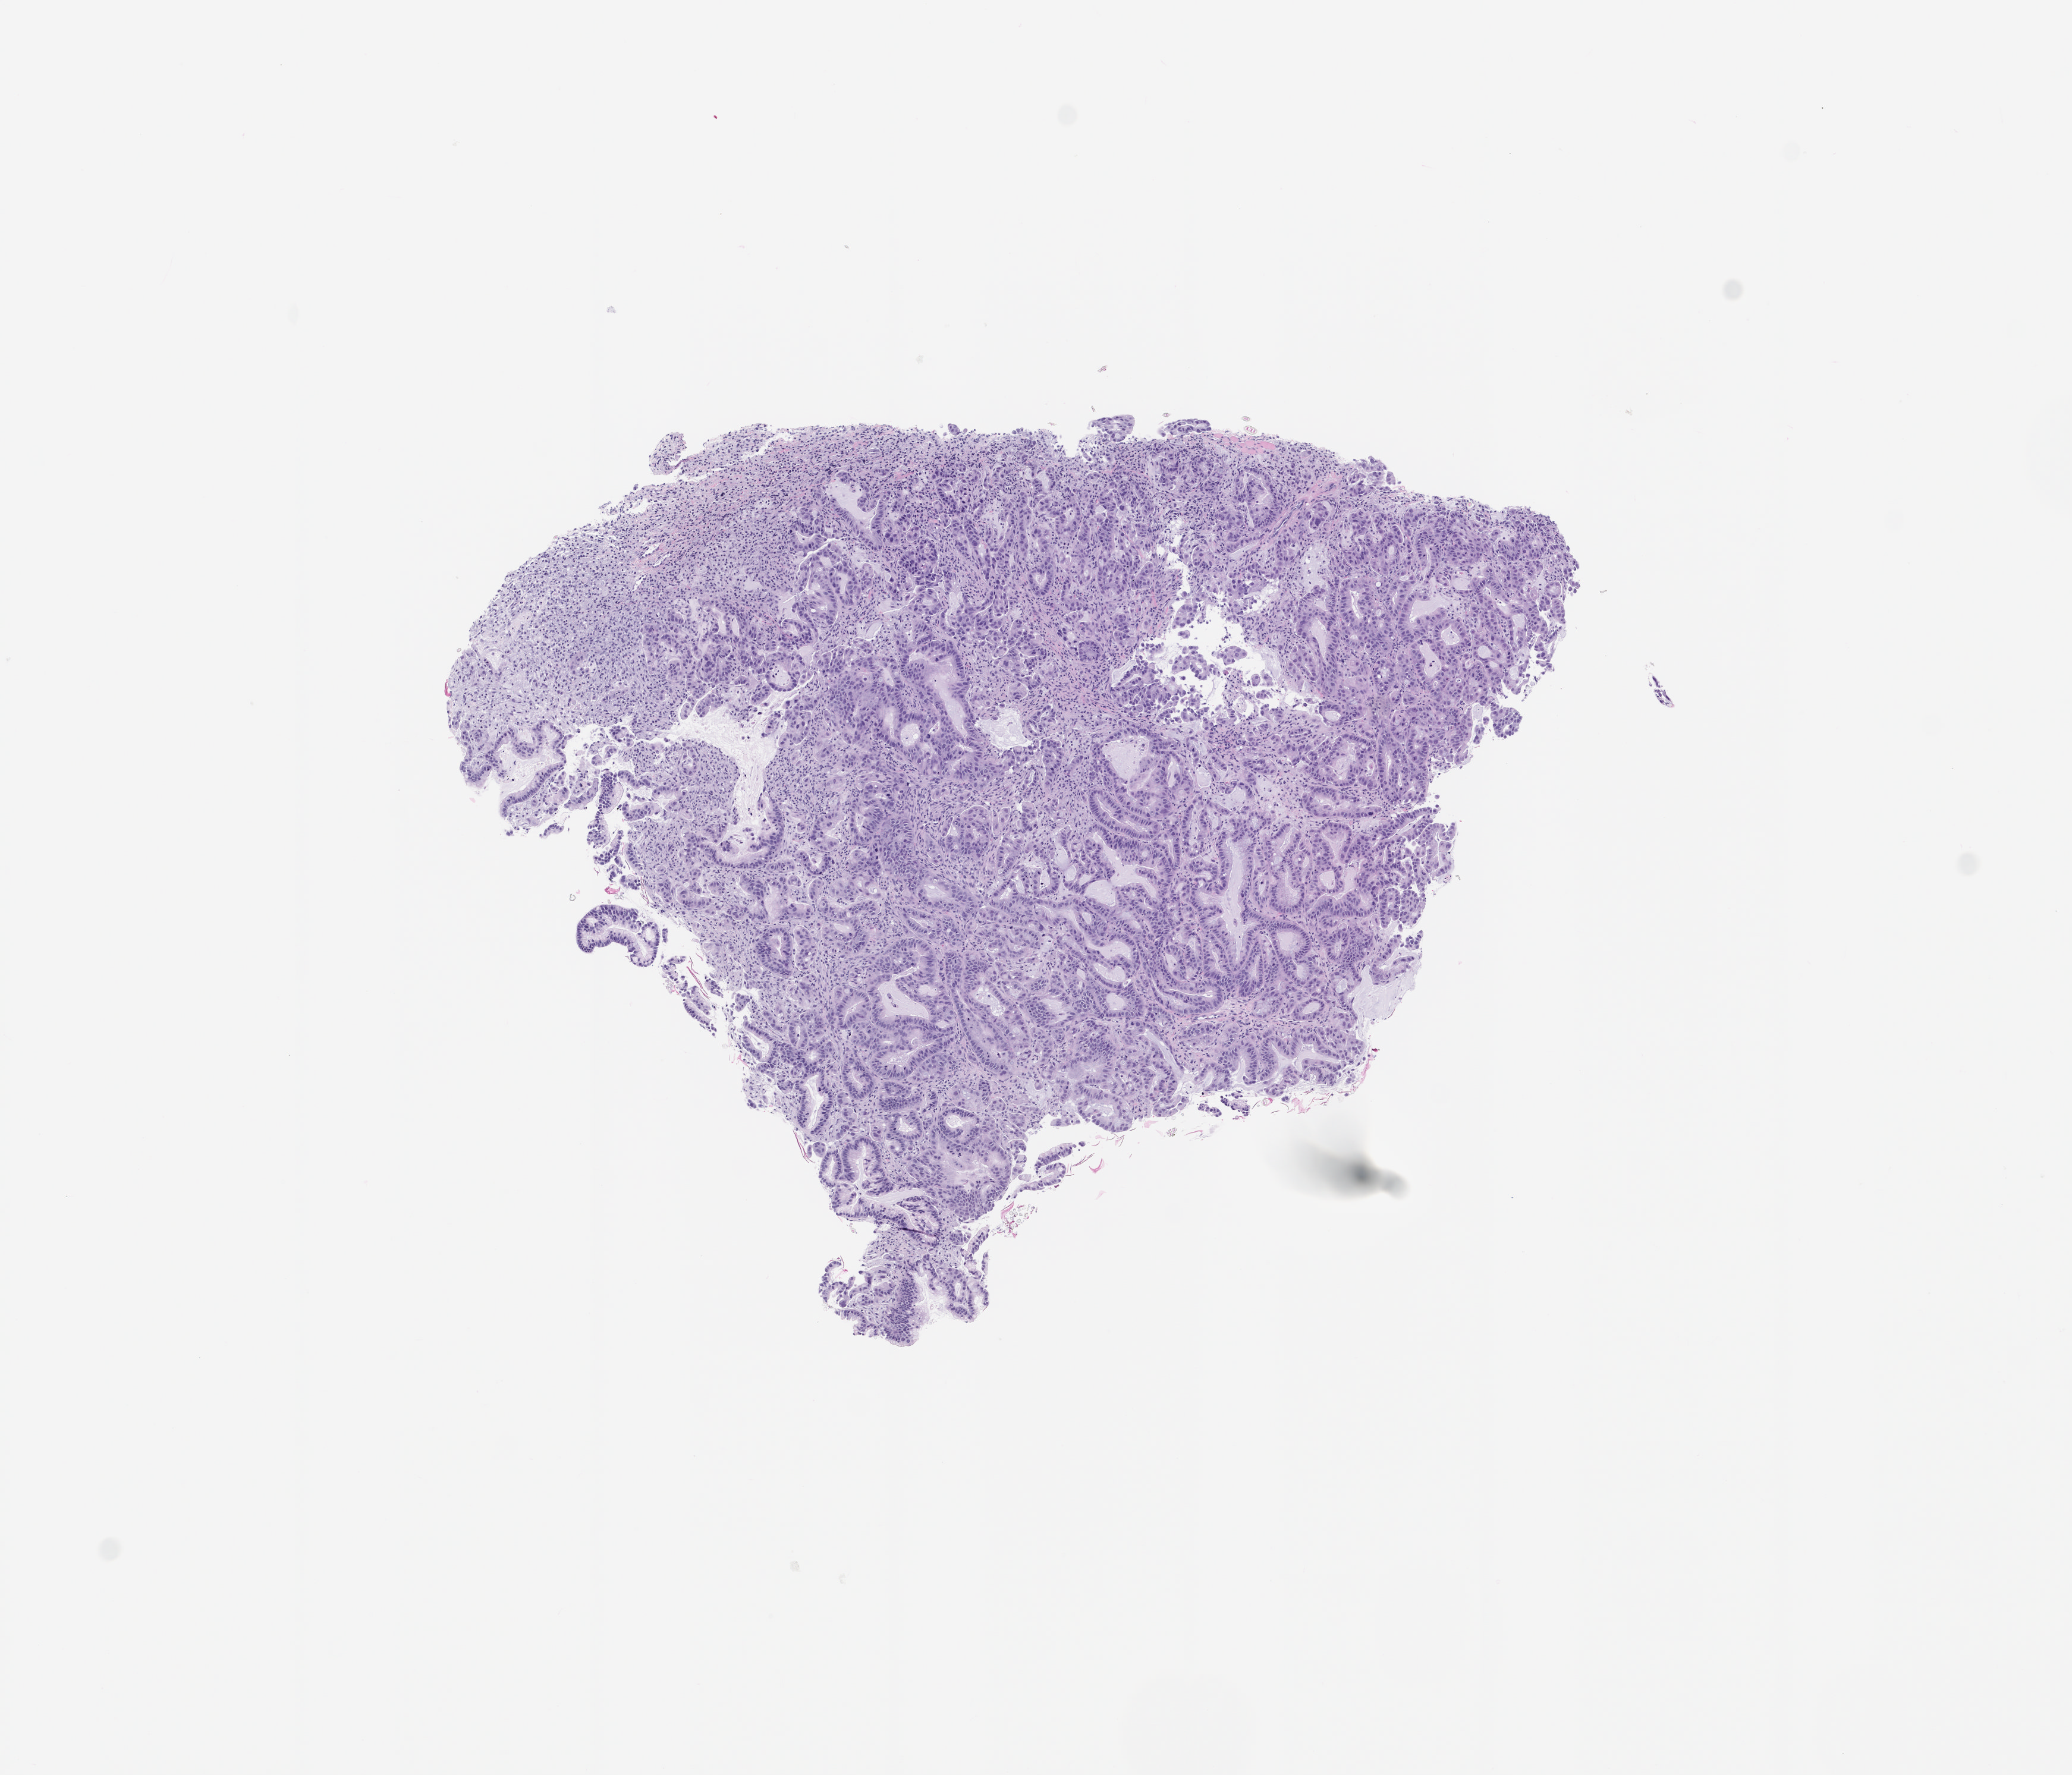
Hematoxylin and eosin (H&E) whole-slide image of a patient-derived xenograft (PDX) tumor grown in a mouse, passage 1 — shown as a low-resolution overview of the whole scanned area (about 7.0 x 6.0 mm), formalin-fixed, paraffin-embedded (FFPE) tissue, tumor site category: pancreas.
Originating patient diagnosis: Pancreatic Adenocarcinoma.